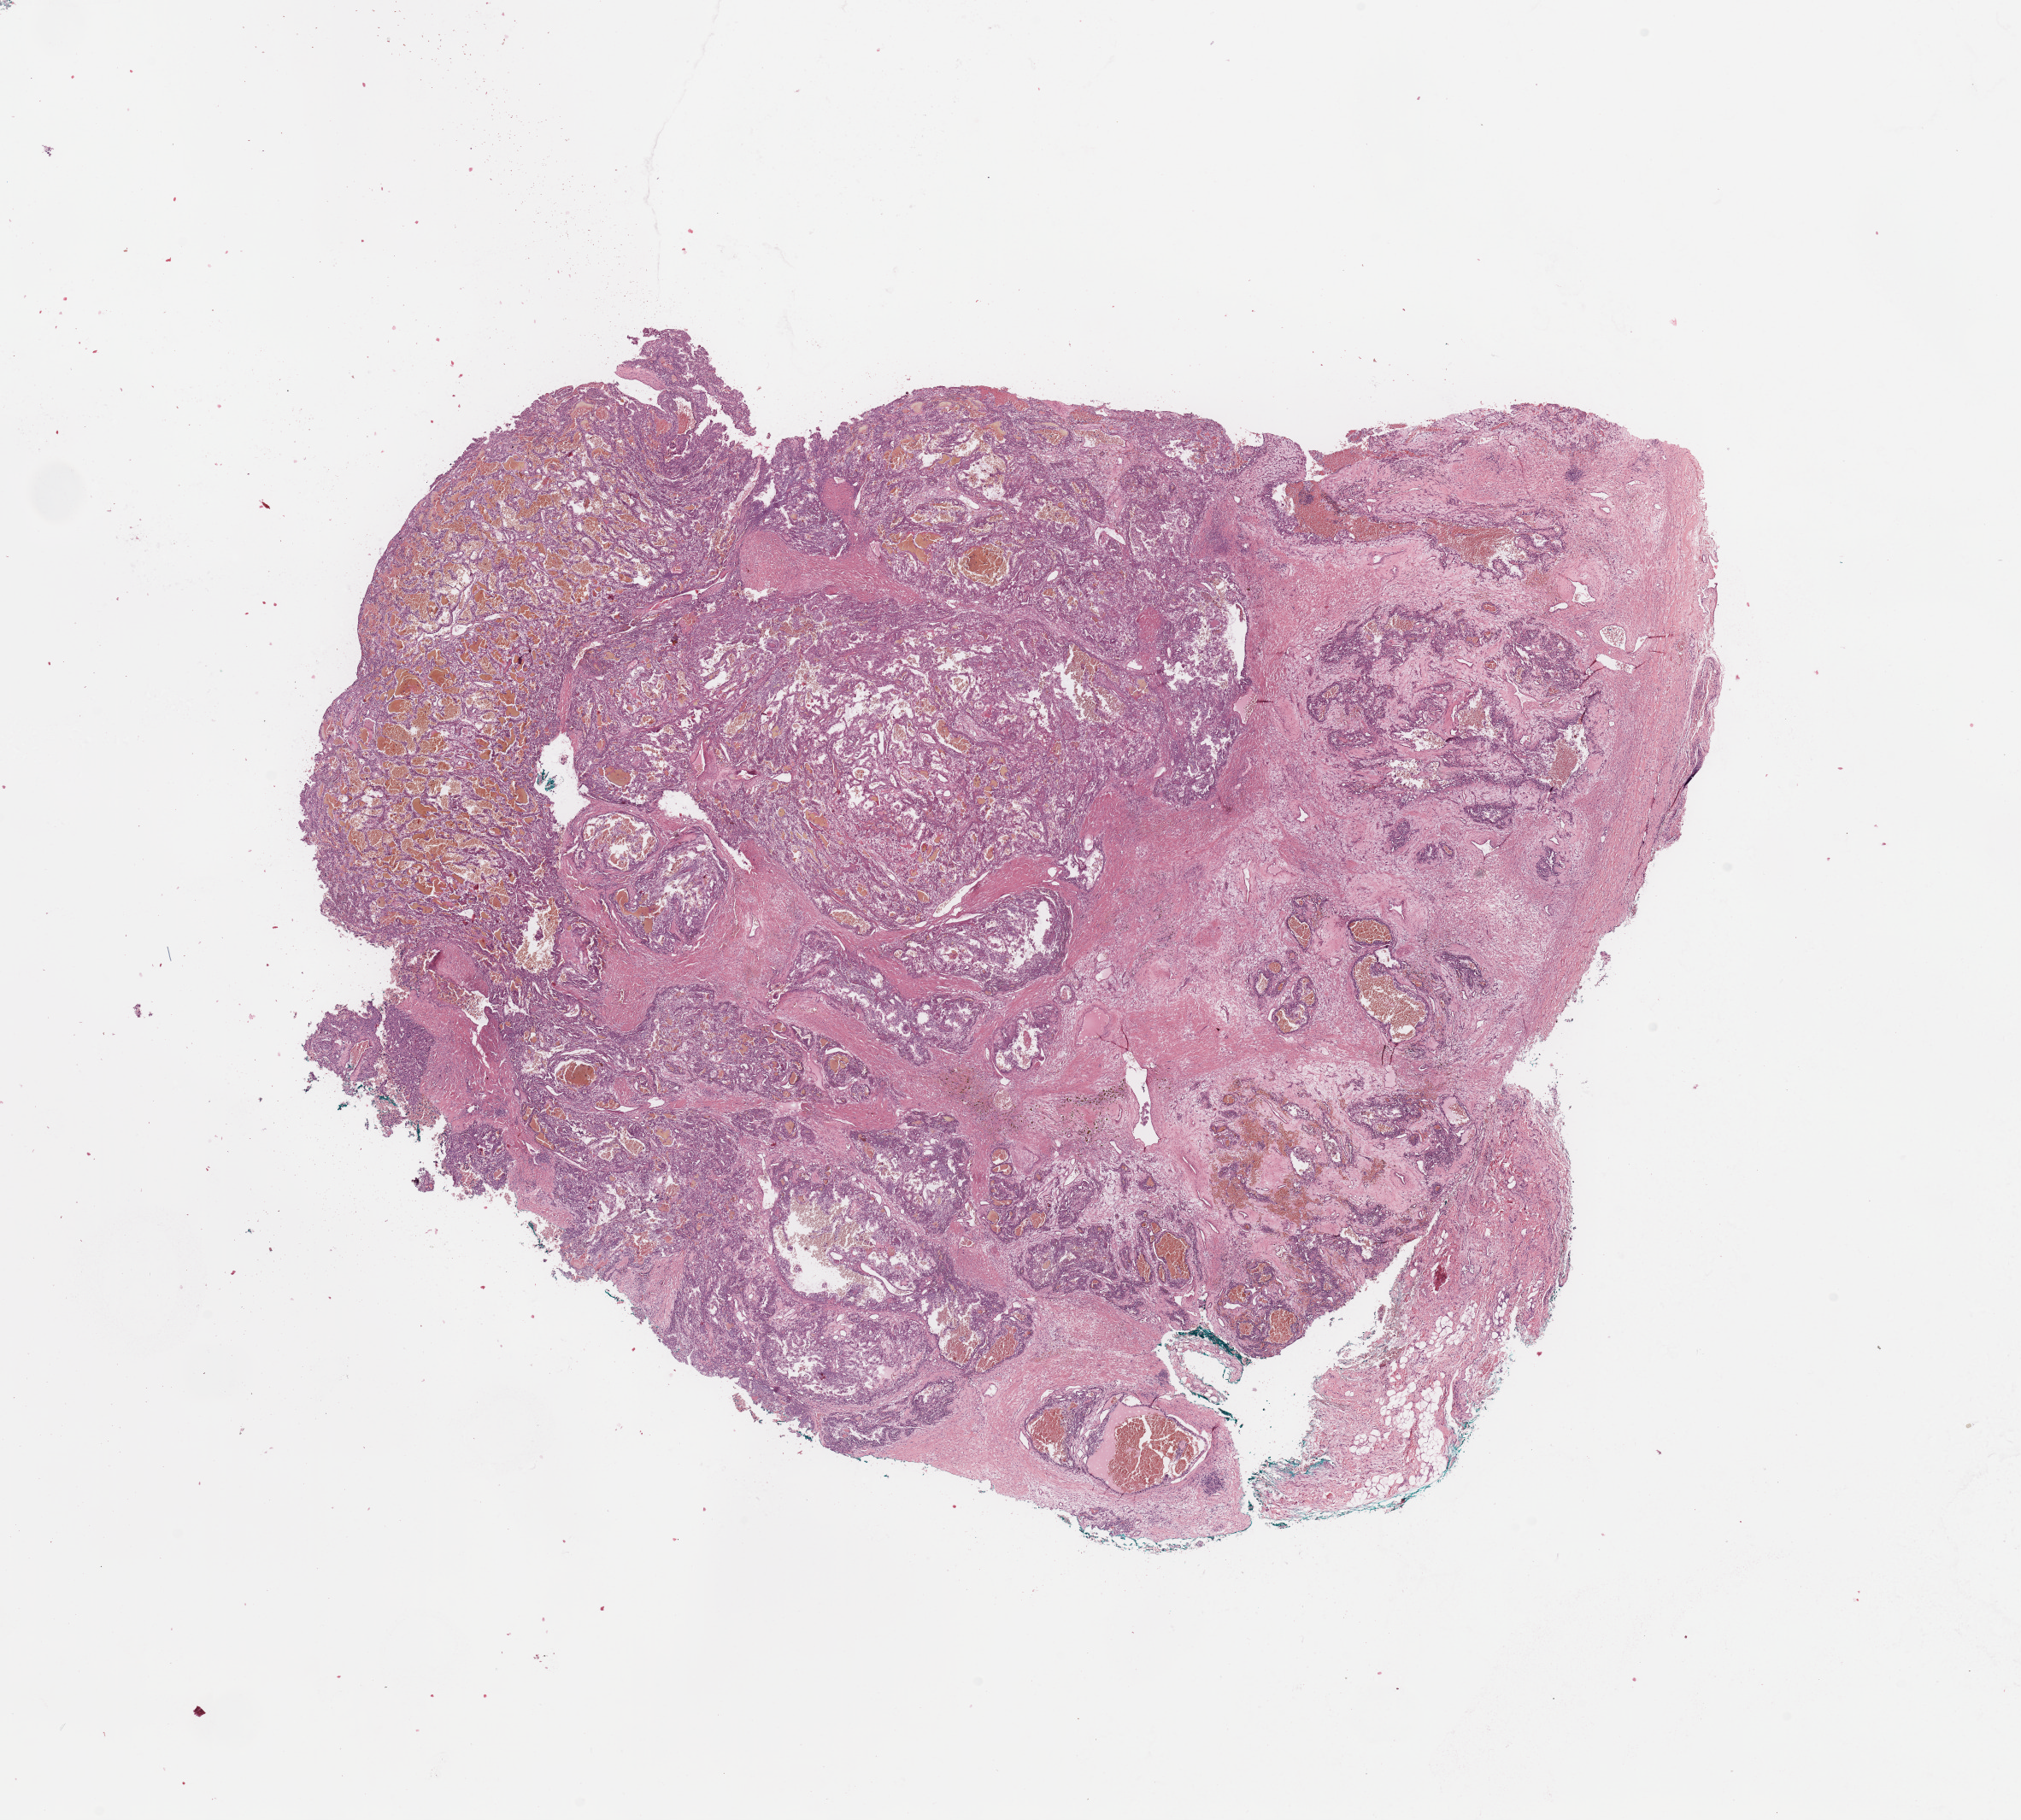
Whole-slide histology image, H&E-stained — a low-resolution overview of the entire scanned area, about 18.7 x 16.8 mm (acquisition: 20x scan), tumour tissue sample, sampled site: kidney. Male, 45 y/o. Histologic grade: G2 (moderately differentiated). Slide review estimates, as recorded: tumour nuclei 80%, necrosis 3%.
• primary tumour site (as recorded): middle
• AJCC pathologic stage: II
• histologic diagnosis: Renal cell carcinoma, NOS